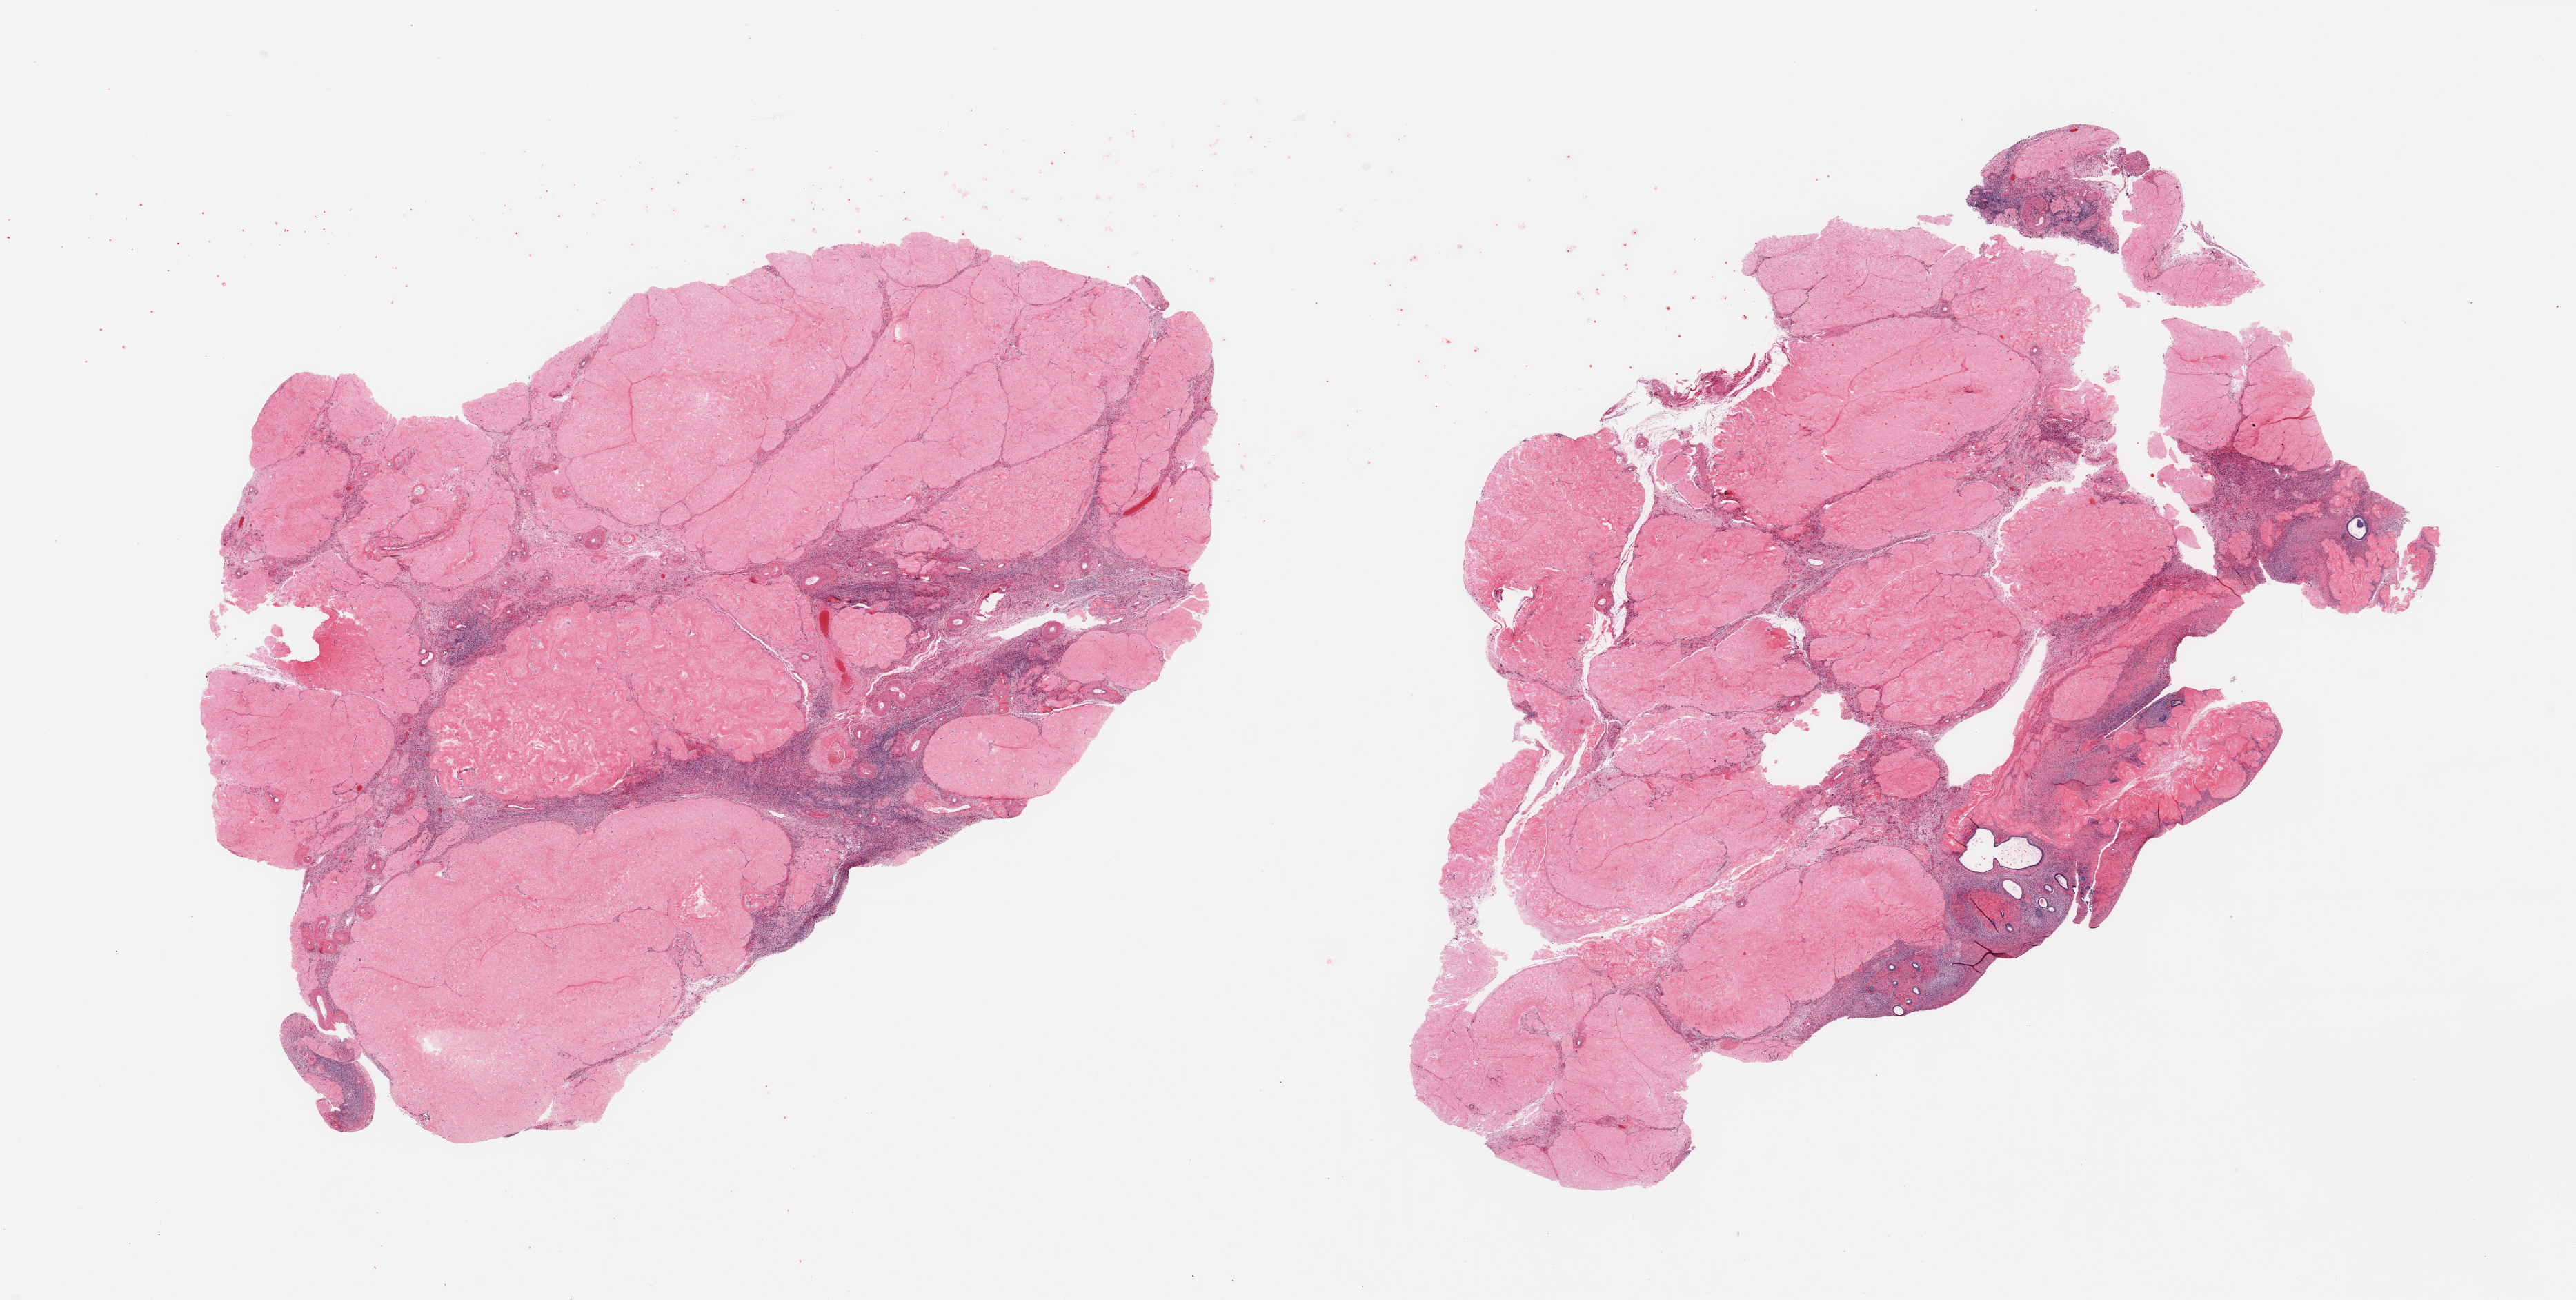
Whole-slide image, H&E stain — shown as a low-resolution overview of the whole scanned area (about 29.5 x 14.9 mm, acquisition: 20x scan); PAXgene-fixed, paraffin-embedded tissue; target tissue: ovary; tissue donor sample. Donor: female.
Reviewer comment on this tissue sample: 2 pieces; corpora albicantia occupy 90%; a few follicles in parenchyma.